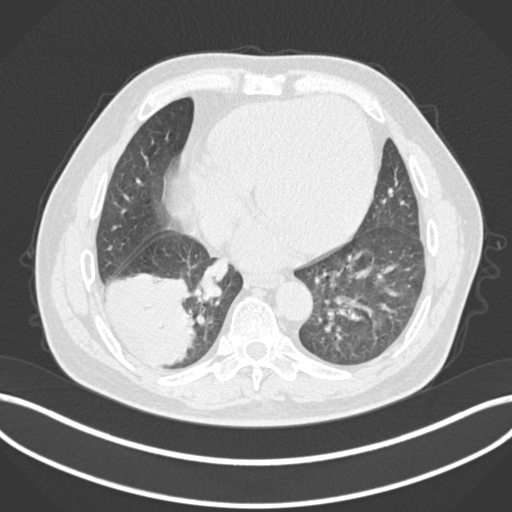
Chest CT, one axial slice; slice 49 of 200 in the series (ordered by position); 120 kVp; lung window (W 1500 / L -600 HU); 1 mm slice thickness; 512 × 512 image matrix. Male patient, age 59 years.
Structures marked on this image (bounding box drawn by a radiologist):
- lung tumour (recorded histology: adenocarcinoma): box from (x=103, y=270) to (x=197, y=370) px